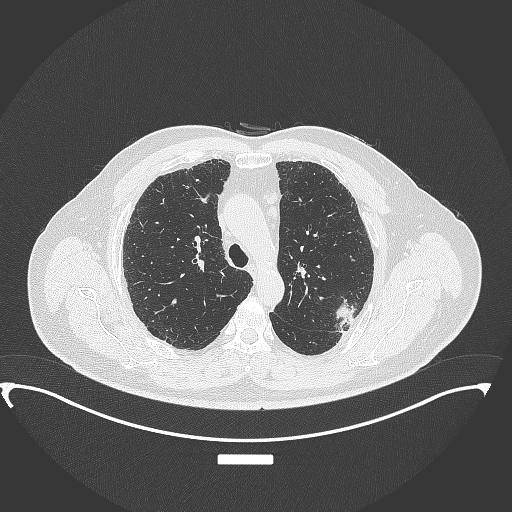
Chest CT, one axial slice. Reconstruction kernel B70f. 120 kVp. Lung window (W 1500 / L -600 HU). 1 mm slice thickness. 512 × 512 image matrix, field of view 459 × 459 mm. Male patient, age 64 years. Case-level facts recorded for this patient, not image findings: clinical TNM (as recorded): T1c N1 M1.
Outlined on this slice (rectangle marked by the reading radiologist):
- lung tumour (recorded histology: adenocarcinoma): bounding box [x1, y1, x2, y2] px = [336, 296, 362, 333]